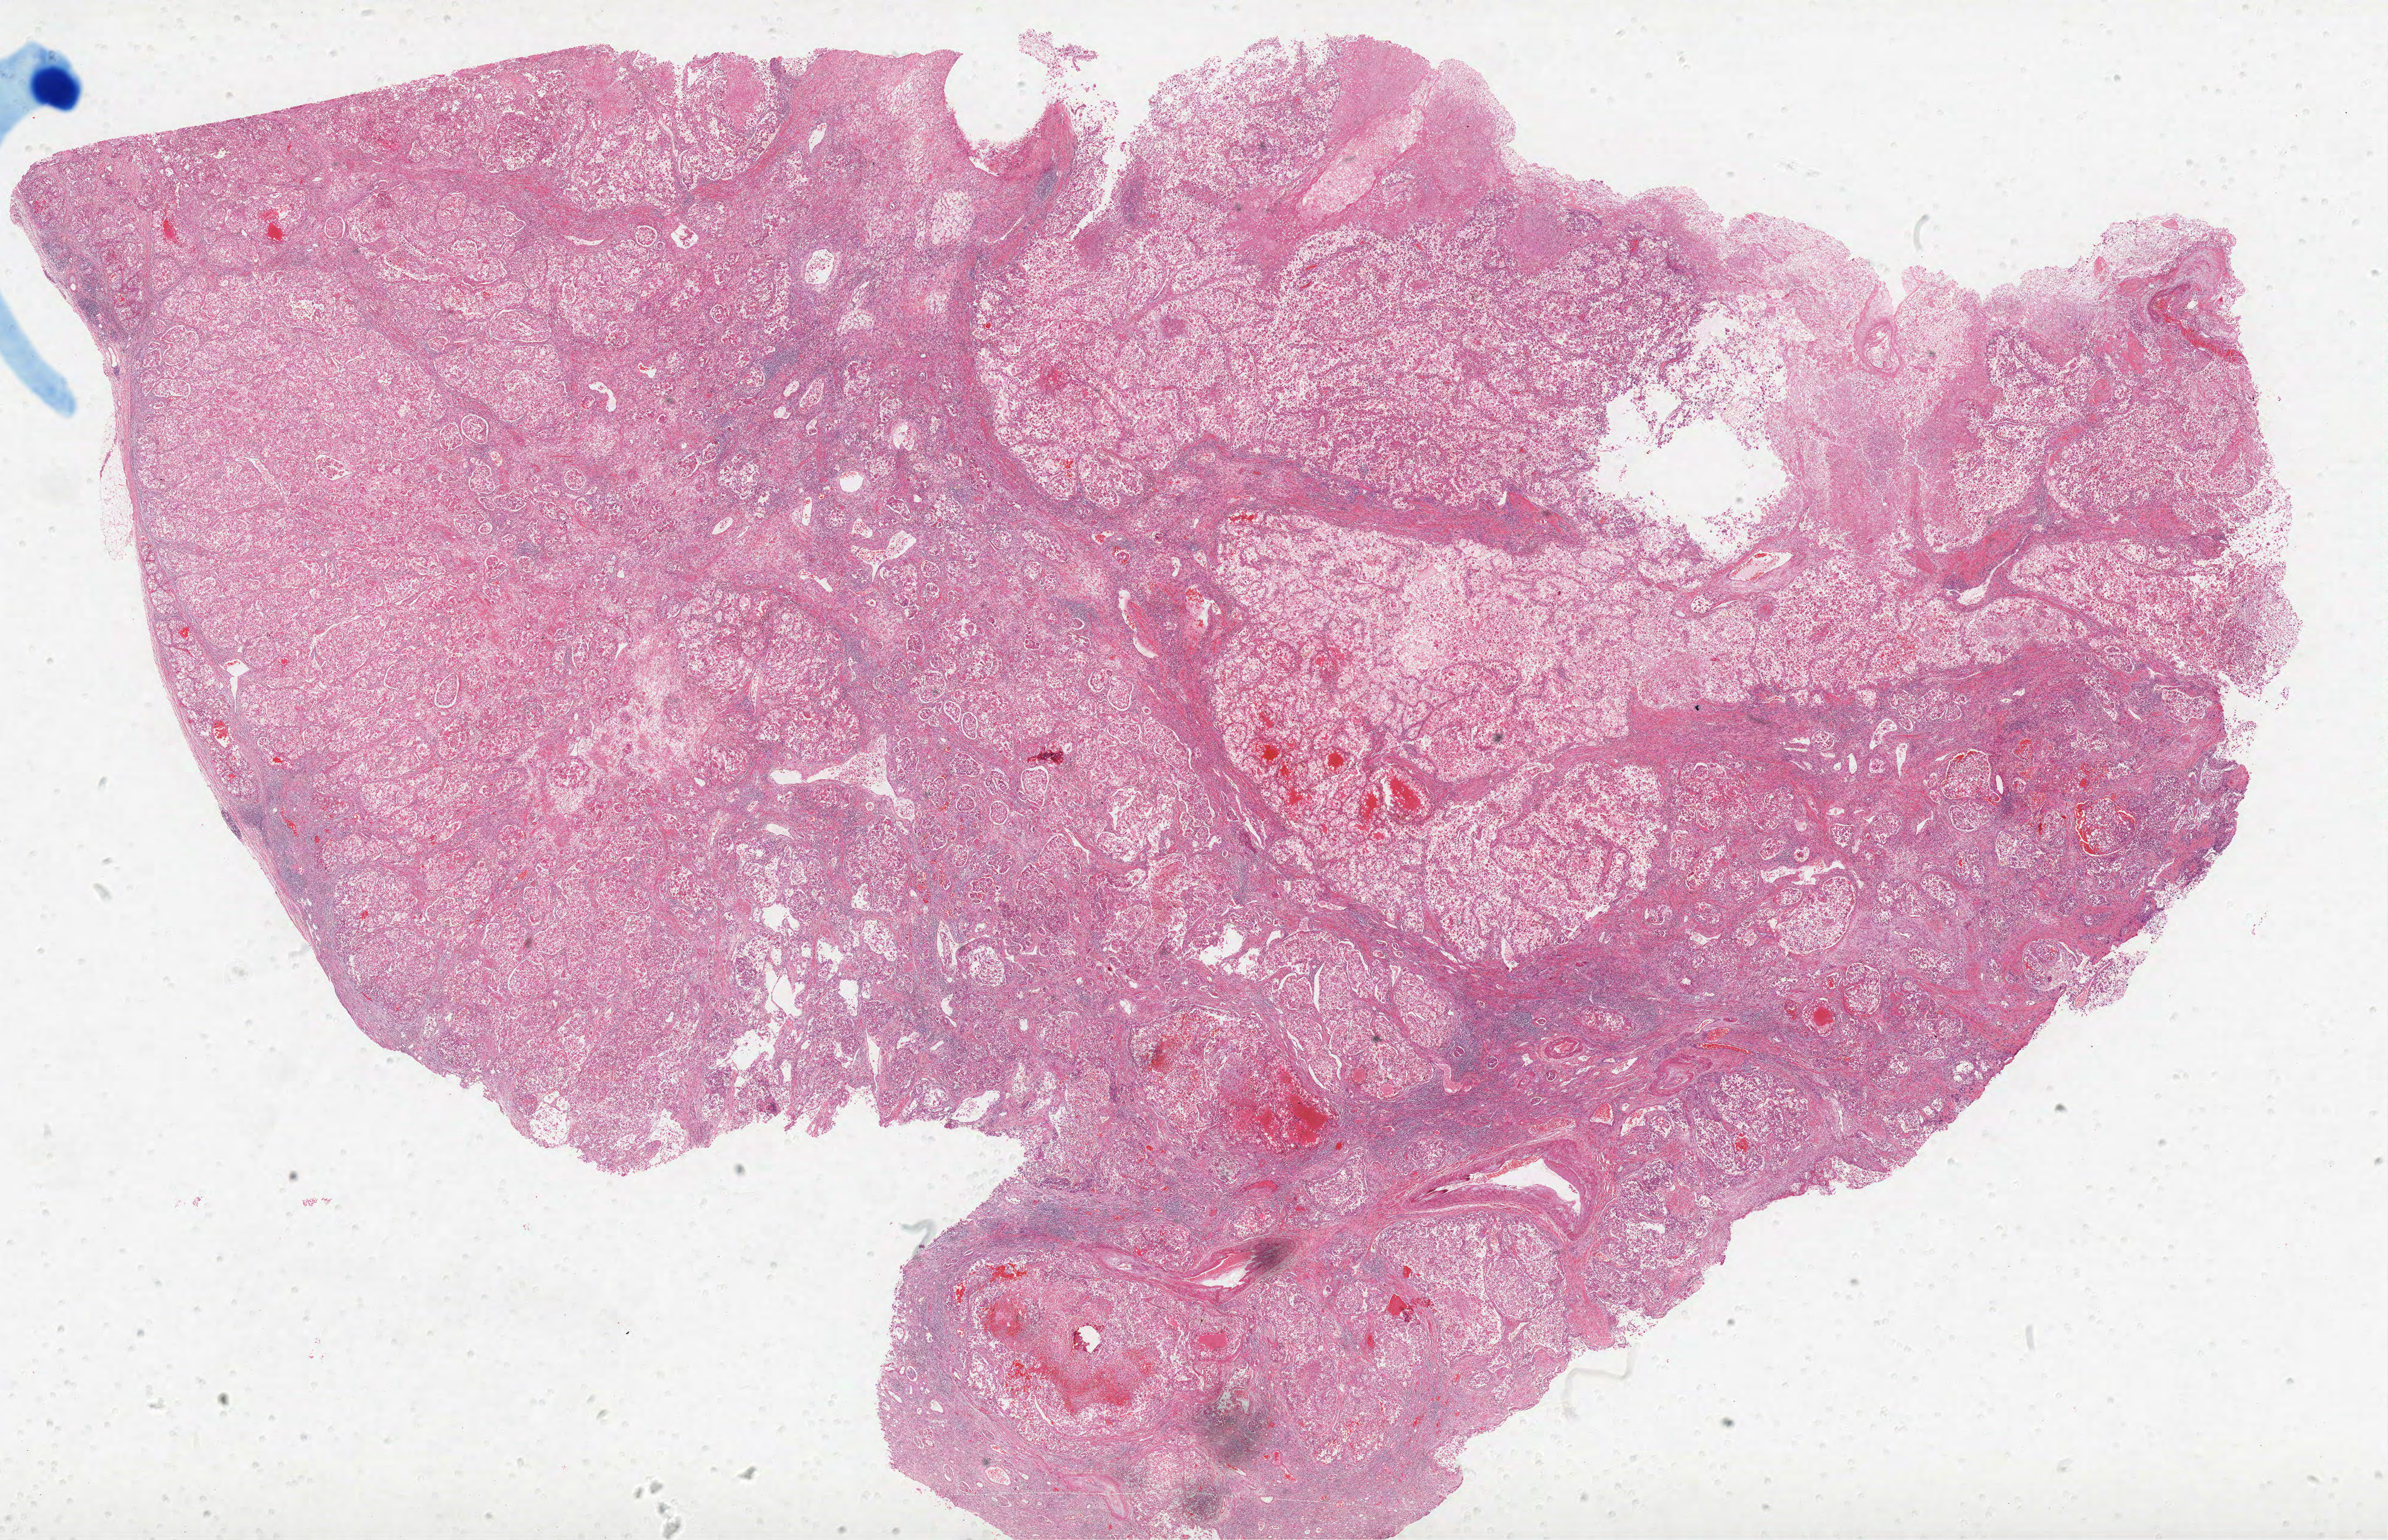
Digitized H&E-stained tissue section (whole slide), low-resolution overview of the scanned area, about 31.6 x 20.4 mm (acquisition: 40x scan). Formalin-fixed paraffin-embedded (FFPE) diagnostic section. Kidney, primary tumour sample. Female, age 76 years at initial diagnosis. Histologic grade: G4 (undifferentiated).
AJCC pathologic stage: III. Lymph nodes positive (case pathology): 0 of 4 examined. Laterality: left. Pathologic diagnosis: Clear cell adenocarcinoma, NOS.